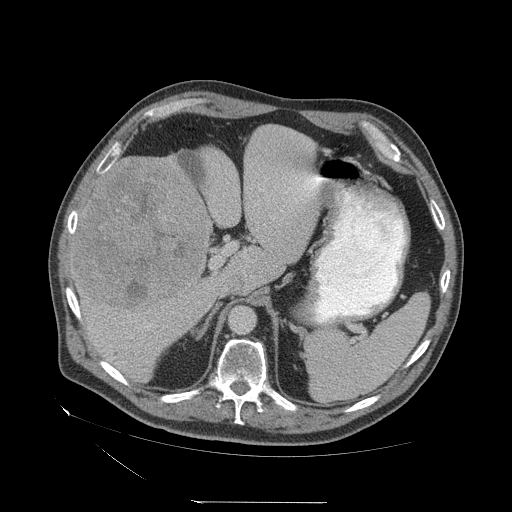
Contrast-enhanced abdominal CT (liver protocol), one axial slice. Position 38 of 83 along the scan axis. Reconstruction kernel STANDARD. Soft-tissue window (W 400 / L 40 HU). 2.5 mm slice thickness. 512 × 512 image matrix. From the clinical record (not read from this slice): diagnosis: hepatocellular carcinoma (patient treated with transarterial chemoembolisation; whether this scan precedes or follows treatment is not stated here); TNM stage (as recorded): Stage-I; Child-Pugh class: A.
Outlined on this slice (semi-automatic segmentation, software-assisted and operator-edited):
- liver parenchyma outside the tumour (the mass and vessels are separate outlines, so this box may not span the whole liver): bounding box (x1, y1, x2, y2) in pixels: (70, 126, 322, 382)
- mass: (73, 158, 209, 310)
- liver vessels: (76, 165, 322, 328)